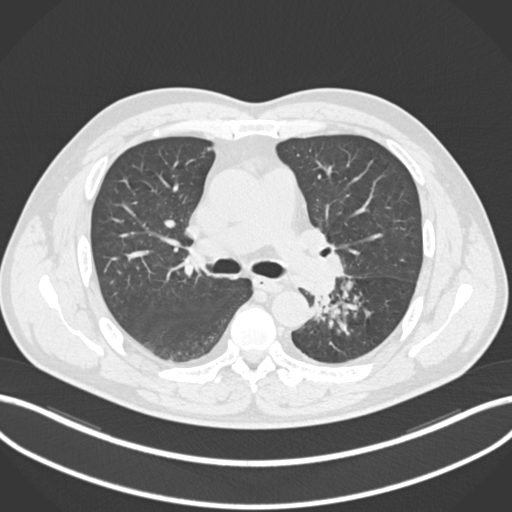
Chest CT, one axial slice; reconstruction kernel B30f; 120 kVp; lung window (W 1500 / L -600 HU); 1 mm slice thickness; 512 × 512 image matrix. Patient: male, 50 years. From the clinical record (not read from this slice): clinical TNM (as recorded): T2a N3 M0.
Structures marked on this image (bounding box drawn by a radiologist):
- lung tumour (recorded histology: squamous cell carcinoma): bounding box (x1, y1, x2, y2) in pixels: (308, 273, 342, 304)